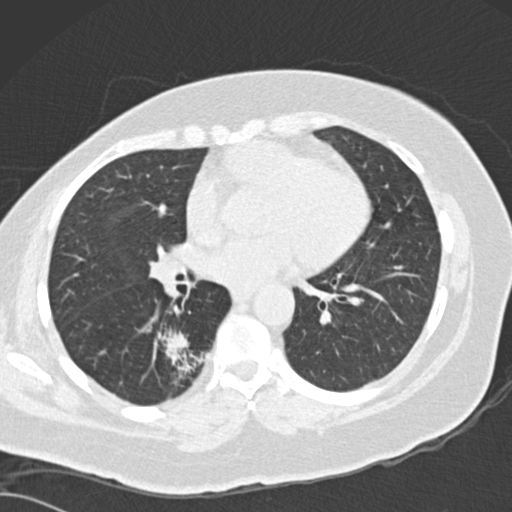
Low-dose screening chest CT, one axial slice. Position 74 of 162 along the scan axis. Reconstruction kernel B30f. 120 kVp. Lung window (W 1500 / L -600 HU). 2 mm slice thickness. 512 × 512 image matrix.
Outlined on this slice (manually delineated by an expert):
- lesion 1 (tumor, lower lobe of right lung): bounding box (x1, y1, x2, y2) in pixels: (160, 329, 204, 379)